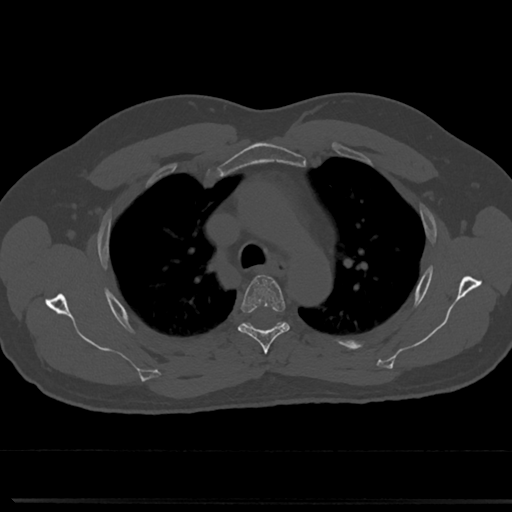
CT including the spine, one axial slice; slice 540 of 817 in the series (ordered by position); reconstruction kernel Br40s/3; 120 kVp; bone window (W 1800 / L 400 HU); 0.5 mm slice thickness; 512 × 512 image matrix. Patient: male, 61 years. Case-level facts recorded for this patient, not image findings: primary cancer: prostate.
Outlined on this slice (semi-automatically segmented with operator editing):
- T4 vertebra: box from (x=237, y=275) to (x=291, y=352) px
- T5 vertebra: (x=247, y=322)–(x=282, y=325)